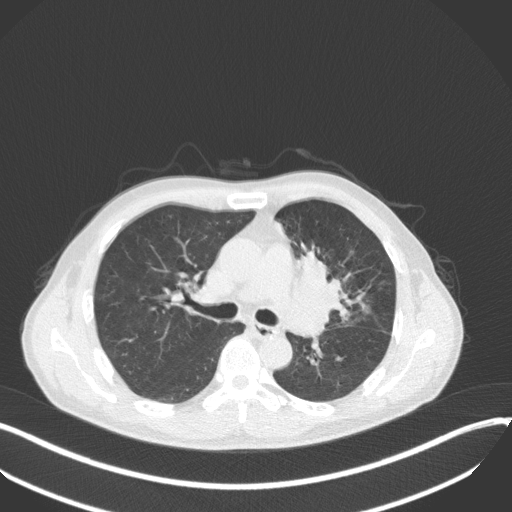
Chest CT, one axial slice; position 207 of 411 along the scan axis; reconstruction kernel B31f; lung window (W 1500 / L -600 HU); 1 mm slice thickness; 512 × 512 image matrix. Patient: male, 56 years. From the clinical record (not read from this slice): clinical TNM (as recorded): T2a N0 M0.
Outlined on this slice (rectangle marked by the reading radiologist):
- lung tumour (recorded histology: squamous cell carcinoma): box from (x=290, y=240) to (x=354, y=325) px